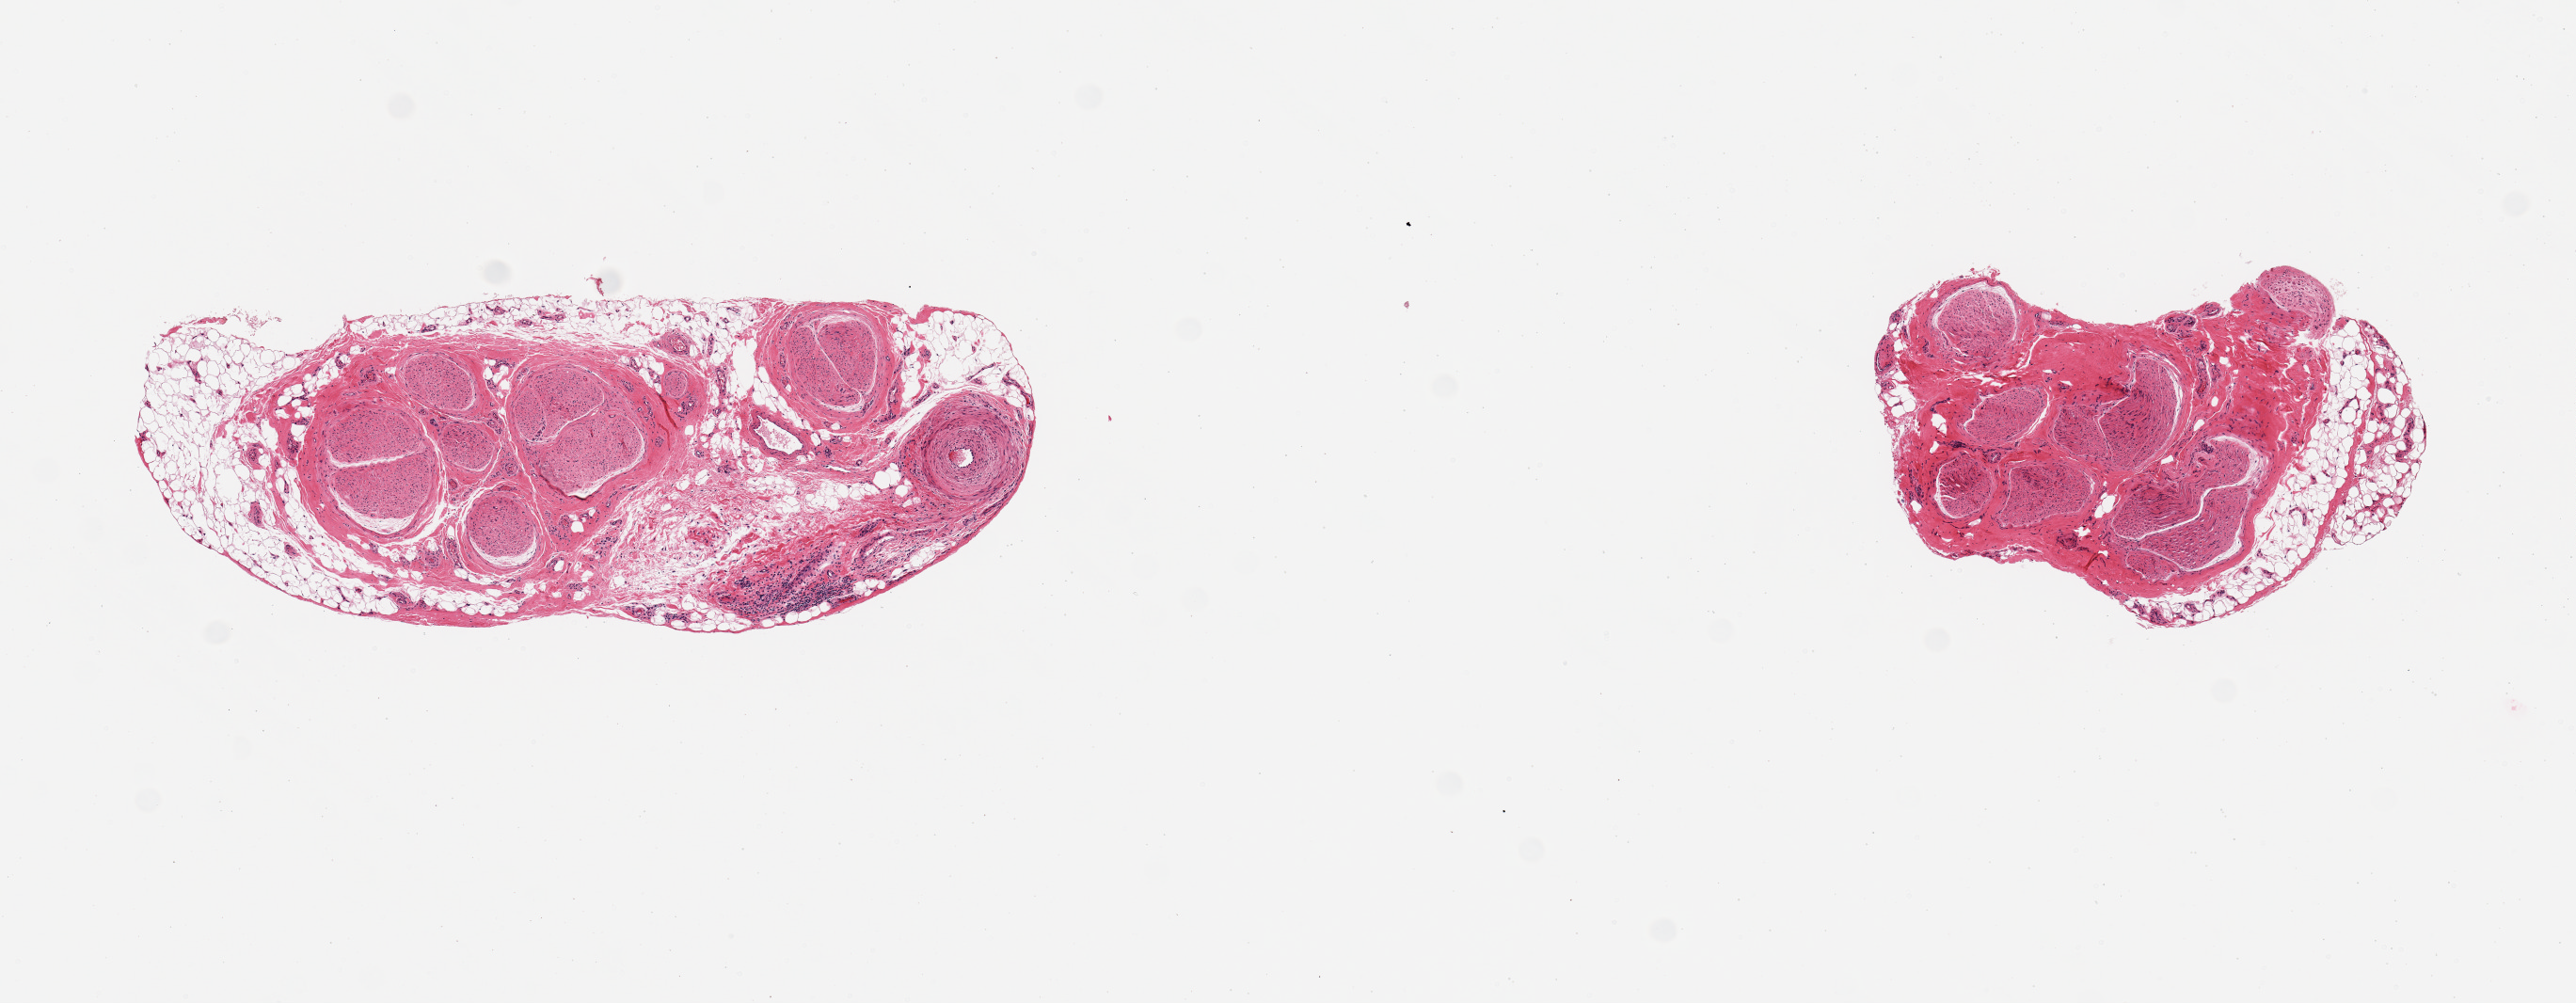
Digitized H&E-stained section, a low-resolution overview of the entire scanned area, about 10.8 x 4.2 mm; PAXgene-fixed paraffin-embedded (PFPE) section; sampled site (target tissue): tibial nerve; donor tissue sample.
- reviewer comment on this tissue sample: 2 pieces; 20% and 50% attached (predominant) and internal fat with focus of chronic inflammation and vessel